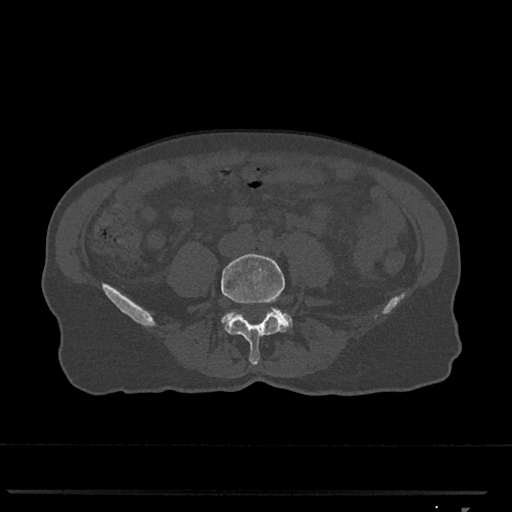
CT including the spine, one axial slice. Bone window (W 1800 / L 400 HU). 0.5 mm slice thickness. 512 × 512 image matrix, field of view 380 × 380 mm. Female patient, age 62 years. From the clinical record (not read from this slice): primary cancer: renal.
Outlined on this slice (semi-automatically segmented with operator editing):
- L4 vertebra: bounding box [x1, y1, x2, y2] px = [221, 254, 287, 365]
- L5 vertebra: [221, 309, 293, 328]